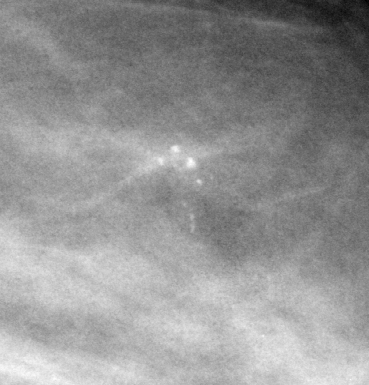
Region of interest cut from a scanned film mammogram (one marked finding); left breast; CC view.
- Finding: calcifications, morphology pleomorphic, distribution clustered; BI-RADS assessment category 5; pathology result (as recorded, not read from the image): malignant.